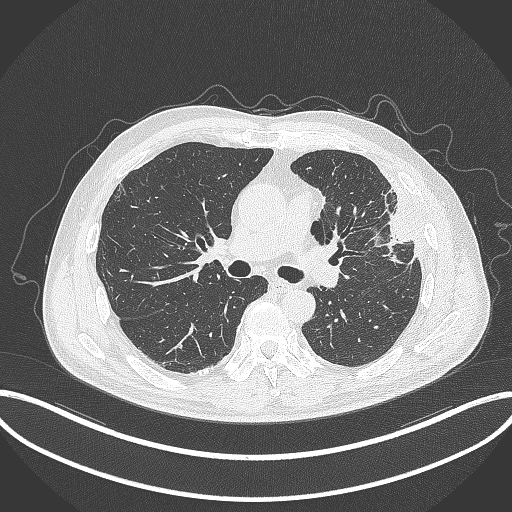
Chest CT, one axial slice; slice 199 of 382 in the series (ordered by position); 120 kVp; lung window (W 1500 / L -600 HU); 1 mm slice thickness; 512 × 512 image matrix, field of view 415 × 415 mm. Patient: male, 64 years. Case-level facts recorded for this patient, not image findings: clinical TNM (as recorded): T4 N1 M0; histopathological grade: G3.
Structures marked on this image (rectangle marked by the reading radiologist):
- lung tumour (recorded histology: adenocarcinoma): bounding box (x1, y1, x2, y2) in pixels: (370, 186, 420, 263)